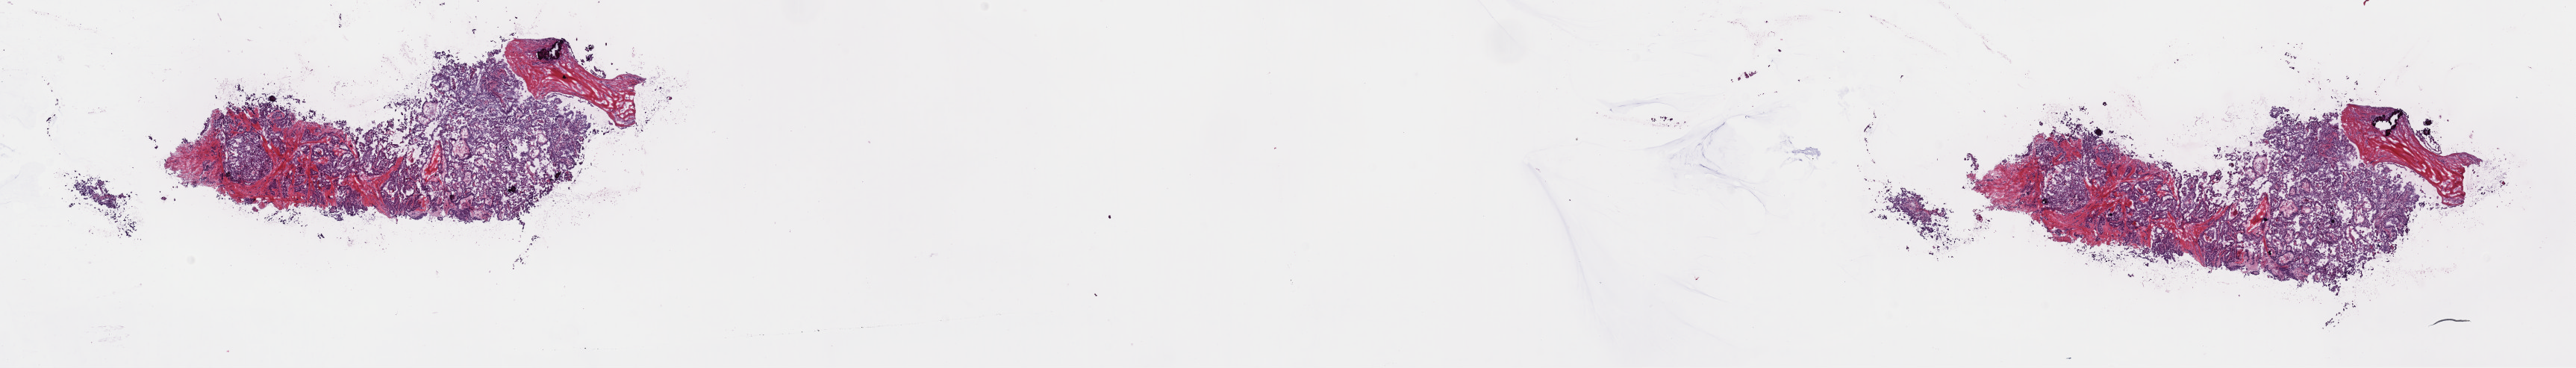
Digitized Hematoxylin and eosin (H&E) stained tissue section (whole slide) — a low-resolution overview of the entire scanned area, about 27.3 x 3.9 mm. Frozen section from the top of the tissue portion. Thyroid, primary tumour sample. Patient: female, age at initial diagnosis 62 years. Slide review estimates, as recorded: tumour cells 95%, tumour nuclei 82%.
Diagnosis: Papillary adenocarcinoma, NOS.